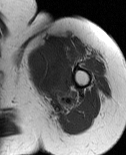
MRI of an extremity soft-tissue mass, one axial slice; slice 59 of 86 in the series (ordered by position); MR volume resampled by the dataset authors to the PET/CT grid (not the native acquisition matrix); 126 × 155 image matrix, field of view 123 × 151 mm. Female patient. From the clinical record (not read from this slice): histological type: pleiomorphic leiomyosarcoma; grade: high; site of the primary tumour: left biceps.
Structures marked on this image (expert contour drawn on MRI and transferred to this co-registered scan by the dataset authors):
- gross tumour volume including surrounding oedema: bounding box <27,42,69,103> (left, top, right, bottom; pixels)
- gross tumour volume (mass): <27,42,69,94>